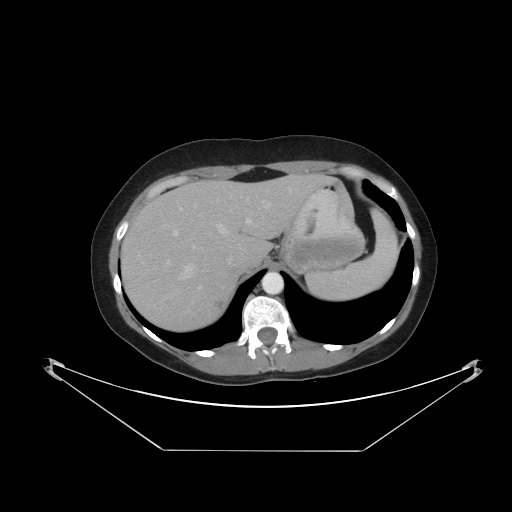
Contrast-enhanced abdominal CT, one axial slice. Slice 35 of 48 in the series (ordered by position). 120 kVp. Intravenous contrast given. Soft-tissue window (W 400 / L 40 HU). 512 × 512 image matrix, field of view 482 × 482 mm. Female patient, age 38 years. From the clinical record (not read from this slice): diagnosis: colorectal cancer liver metastases, imaged before liver resection; multiple liver metastases: yes; largest metastasis: 2.5 cm; disease in both lobes: no.
Structures marked on this image (expert manual segmentation):
- hepatic veins: bounding box (x1, y1, x2, y2) in pixels: (182, 197, 261, 278)
- liver: (121, 177, 351, 334)
- planned liver remnant (the part of the liver to remain after resection): (188, 177, 351, 257)
- portal vein (with intrahepatic branches): (173, 189, 291, 289)
- liver metastasis: (213, 297, 229, 313)